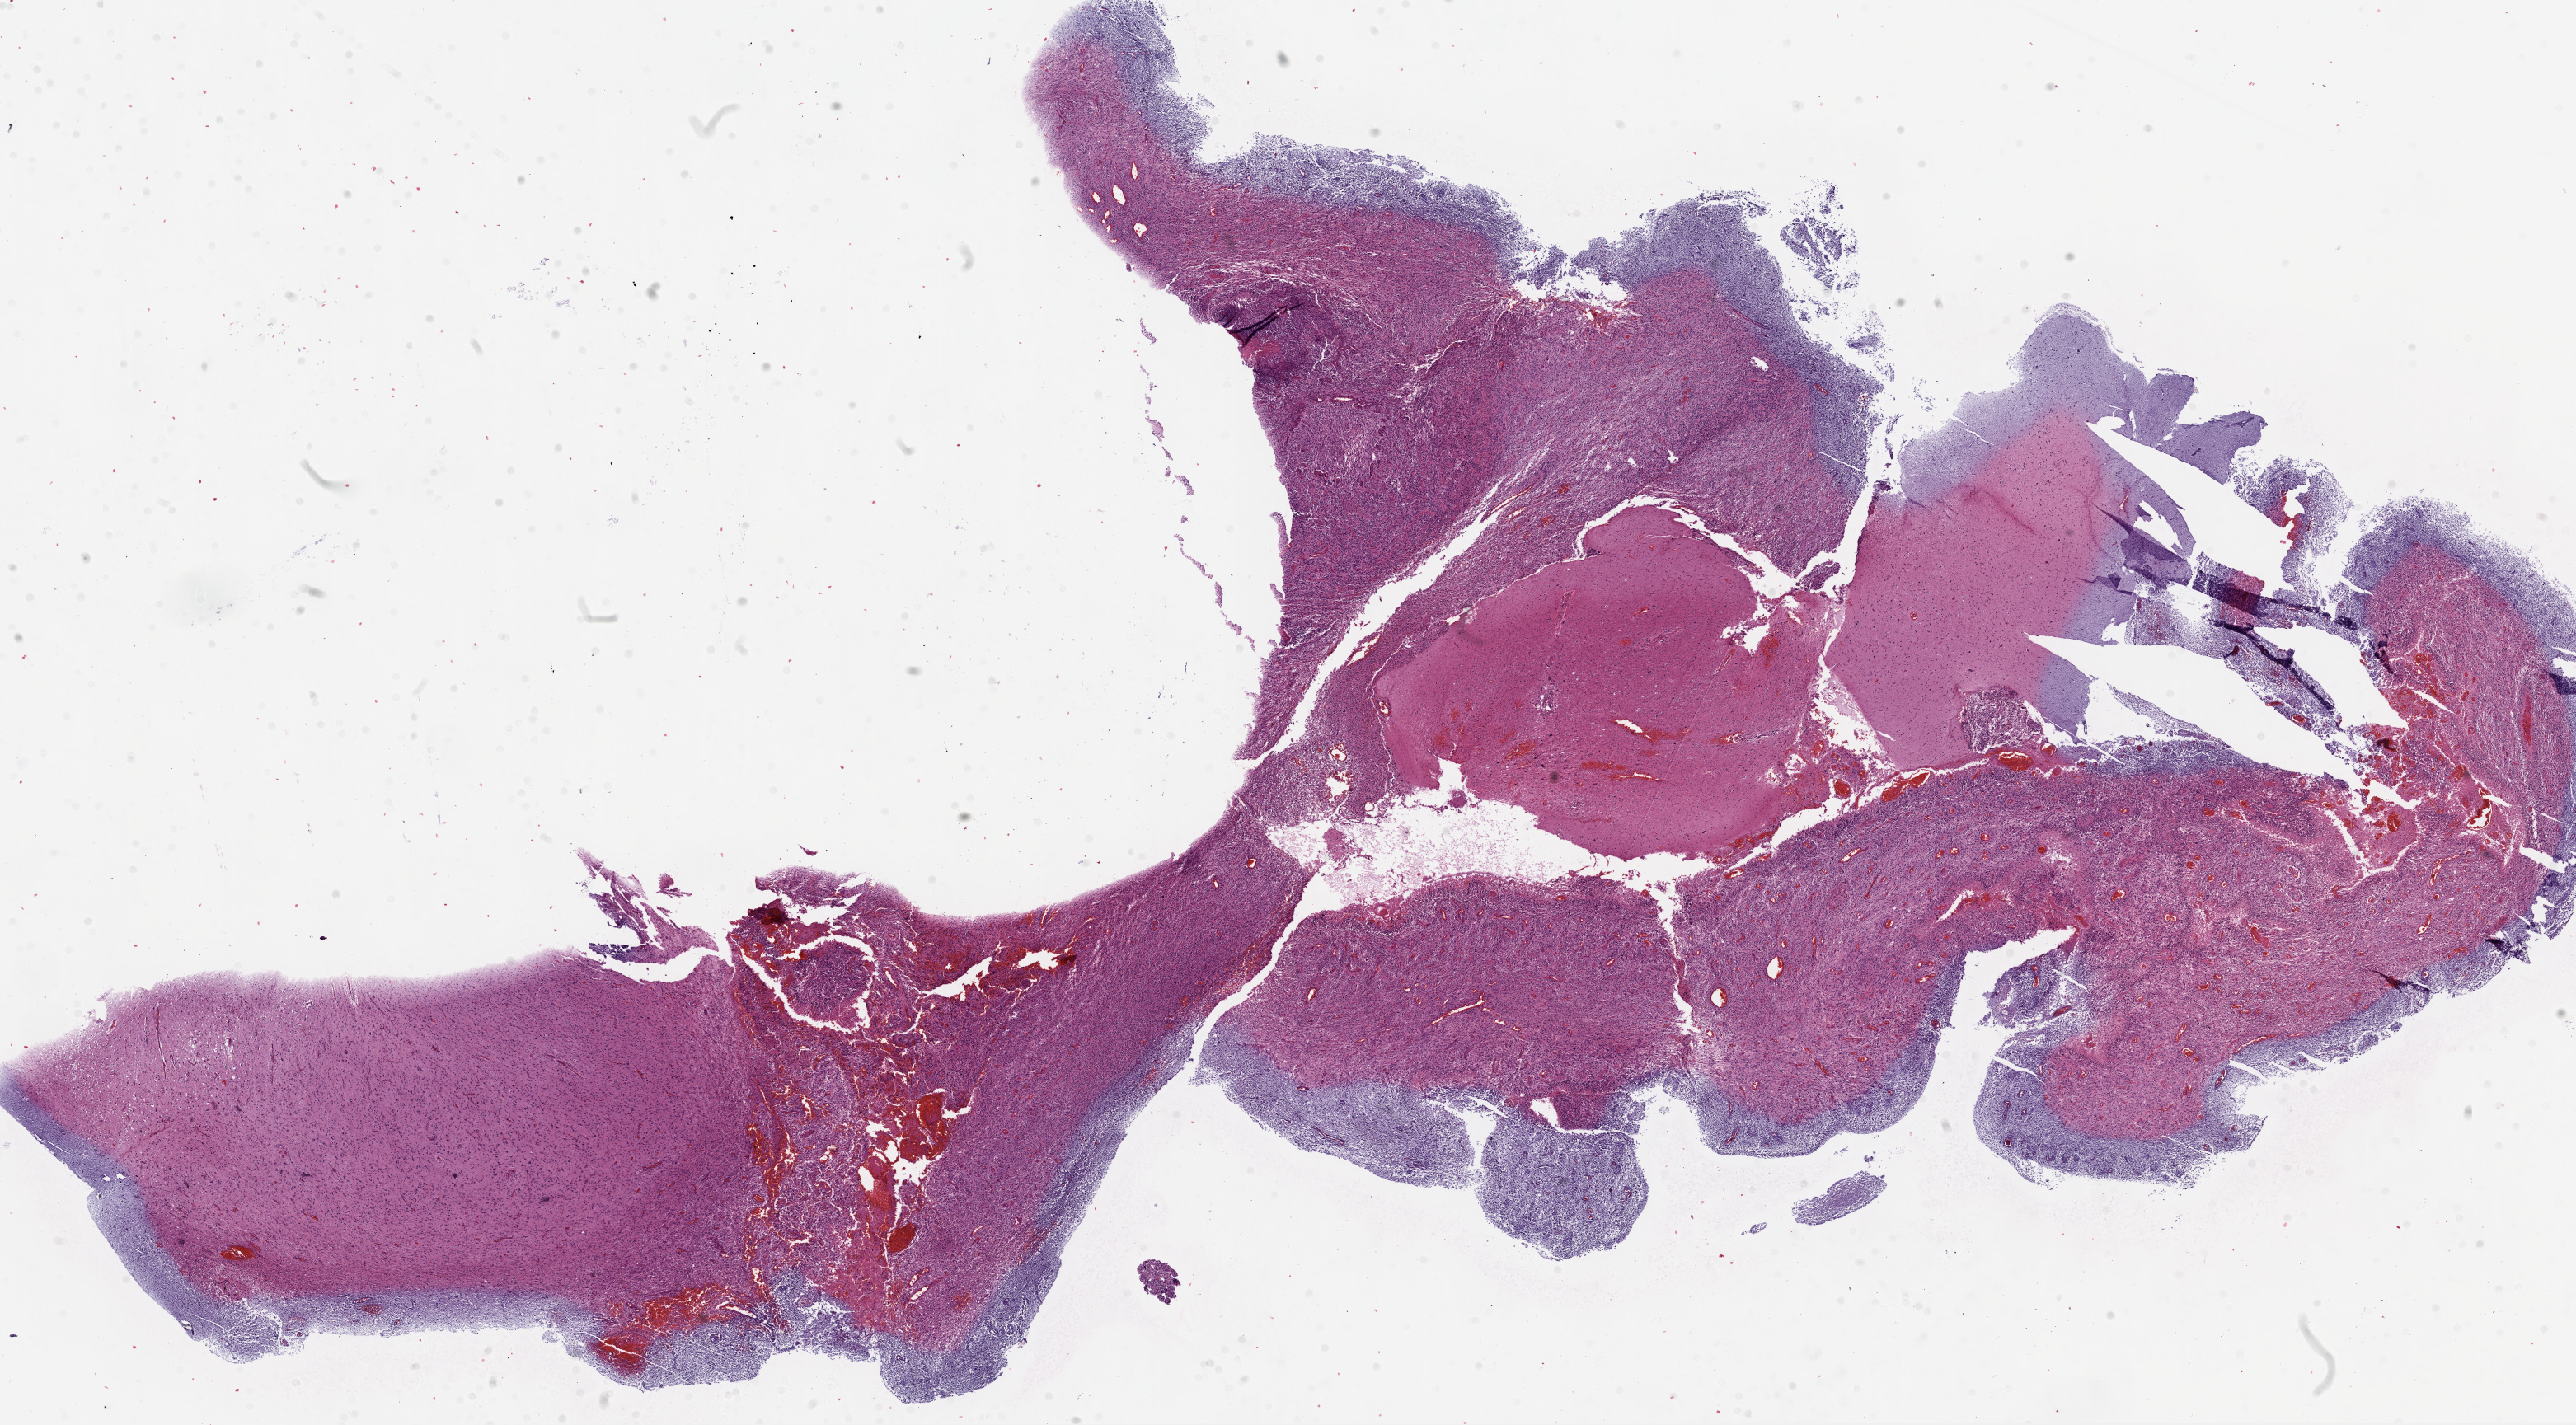
H&E-stained whole-slide image — a low-resolution overview of the entire scanned area, about 25.1 x 13.9 mm (from a 20x scan), formalin-fixed paraffin-embedded (FFPE) diagnostic section, sample: primary tumour, brain. Patient: male, age at initial diagnosis 14 years.
Pathologic diagnosis: Glioblastoma.